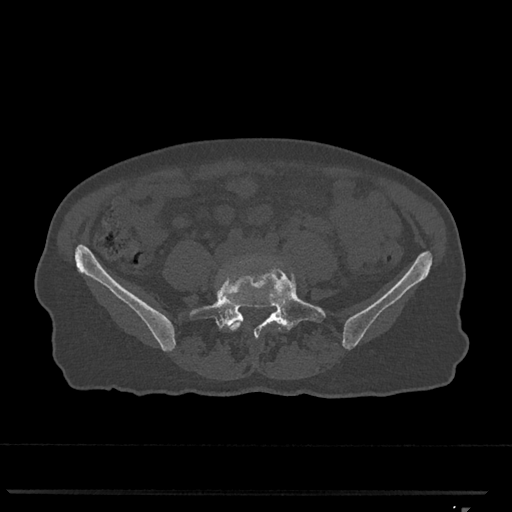
CT including the spine, one axial slice. Slice 167 of 793 in the series (ordered by position). Reconstruction kernel Br40s/3. Bone window (W 1800 / L 400 HU). 0.5 mm slice thickness. 512 × 512 image matrix, field of view 380 × 380 mm. Female patient, age 62 years. Case-level facts recorded for this patient, not image findings: primary cancer: renal.
Outlined on this slice (semi-automatically segmented with operator editing):
- L4 vertebra: bounding box [x1, y1, x2, y2] px = [217, 256, 282, 331]
- L5 vertebra: [189, 262, 326, 337]